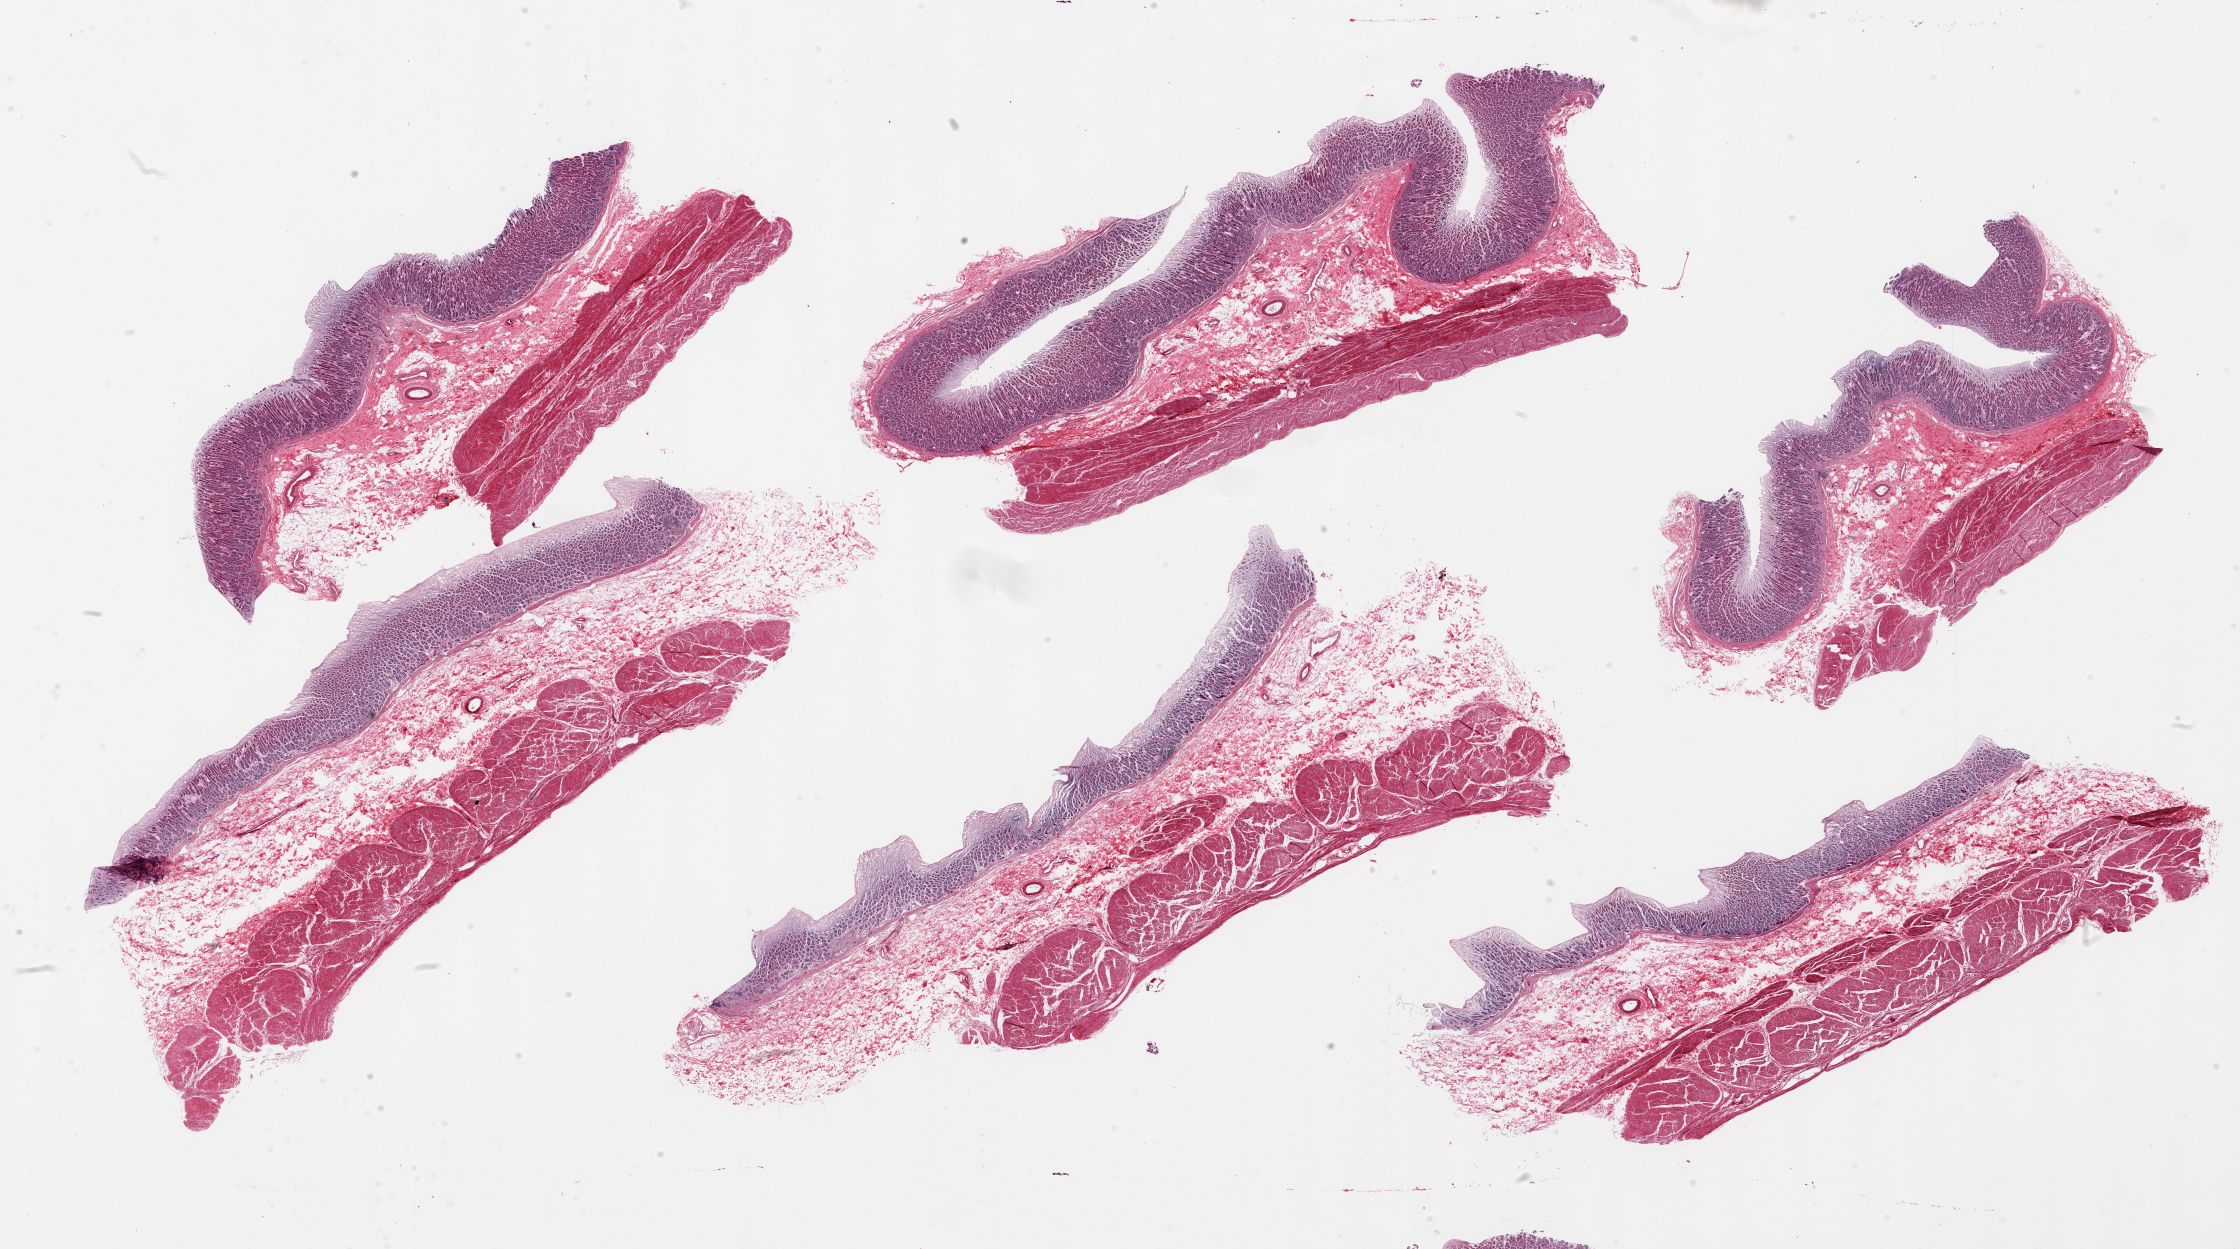
H&E whole-slide image, brightfield — a low-resolution overview of the entire scanned area, about 35.4 x 19.8 mm (from a 20x scan). PAXgene-fixed, paraffin-embedded tissue. Section of stomach (target tissue). Donor tissue sample.
Pathologist's review note for this sample: 6 pieces; full thickness sections, moderate to severe mucosal autolysis.